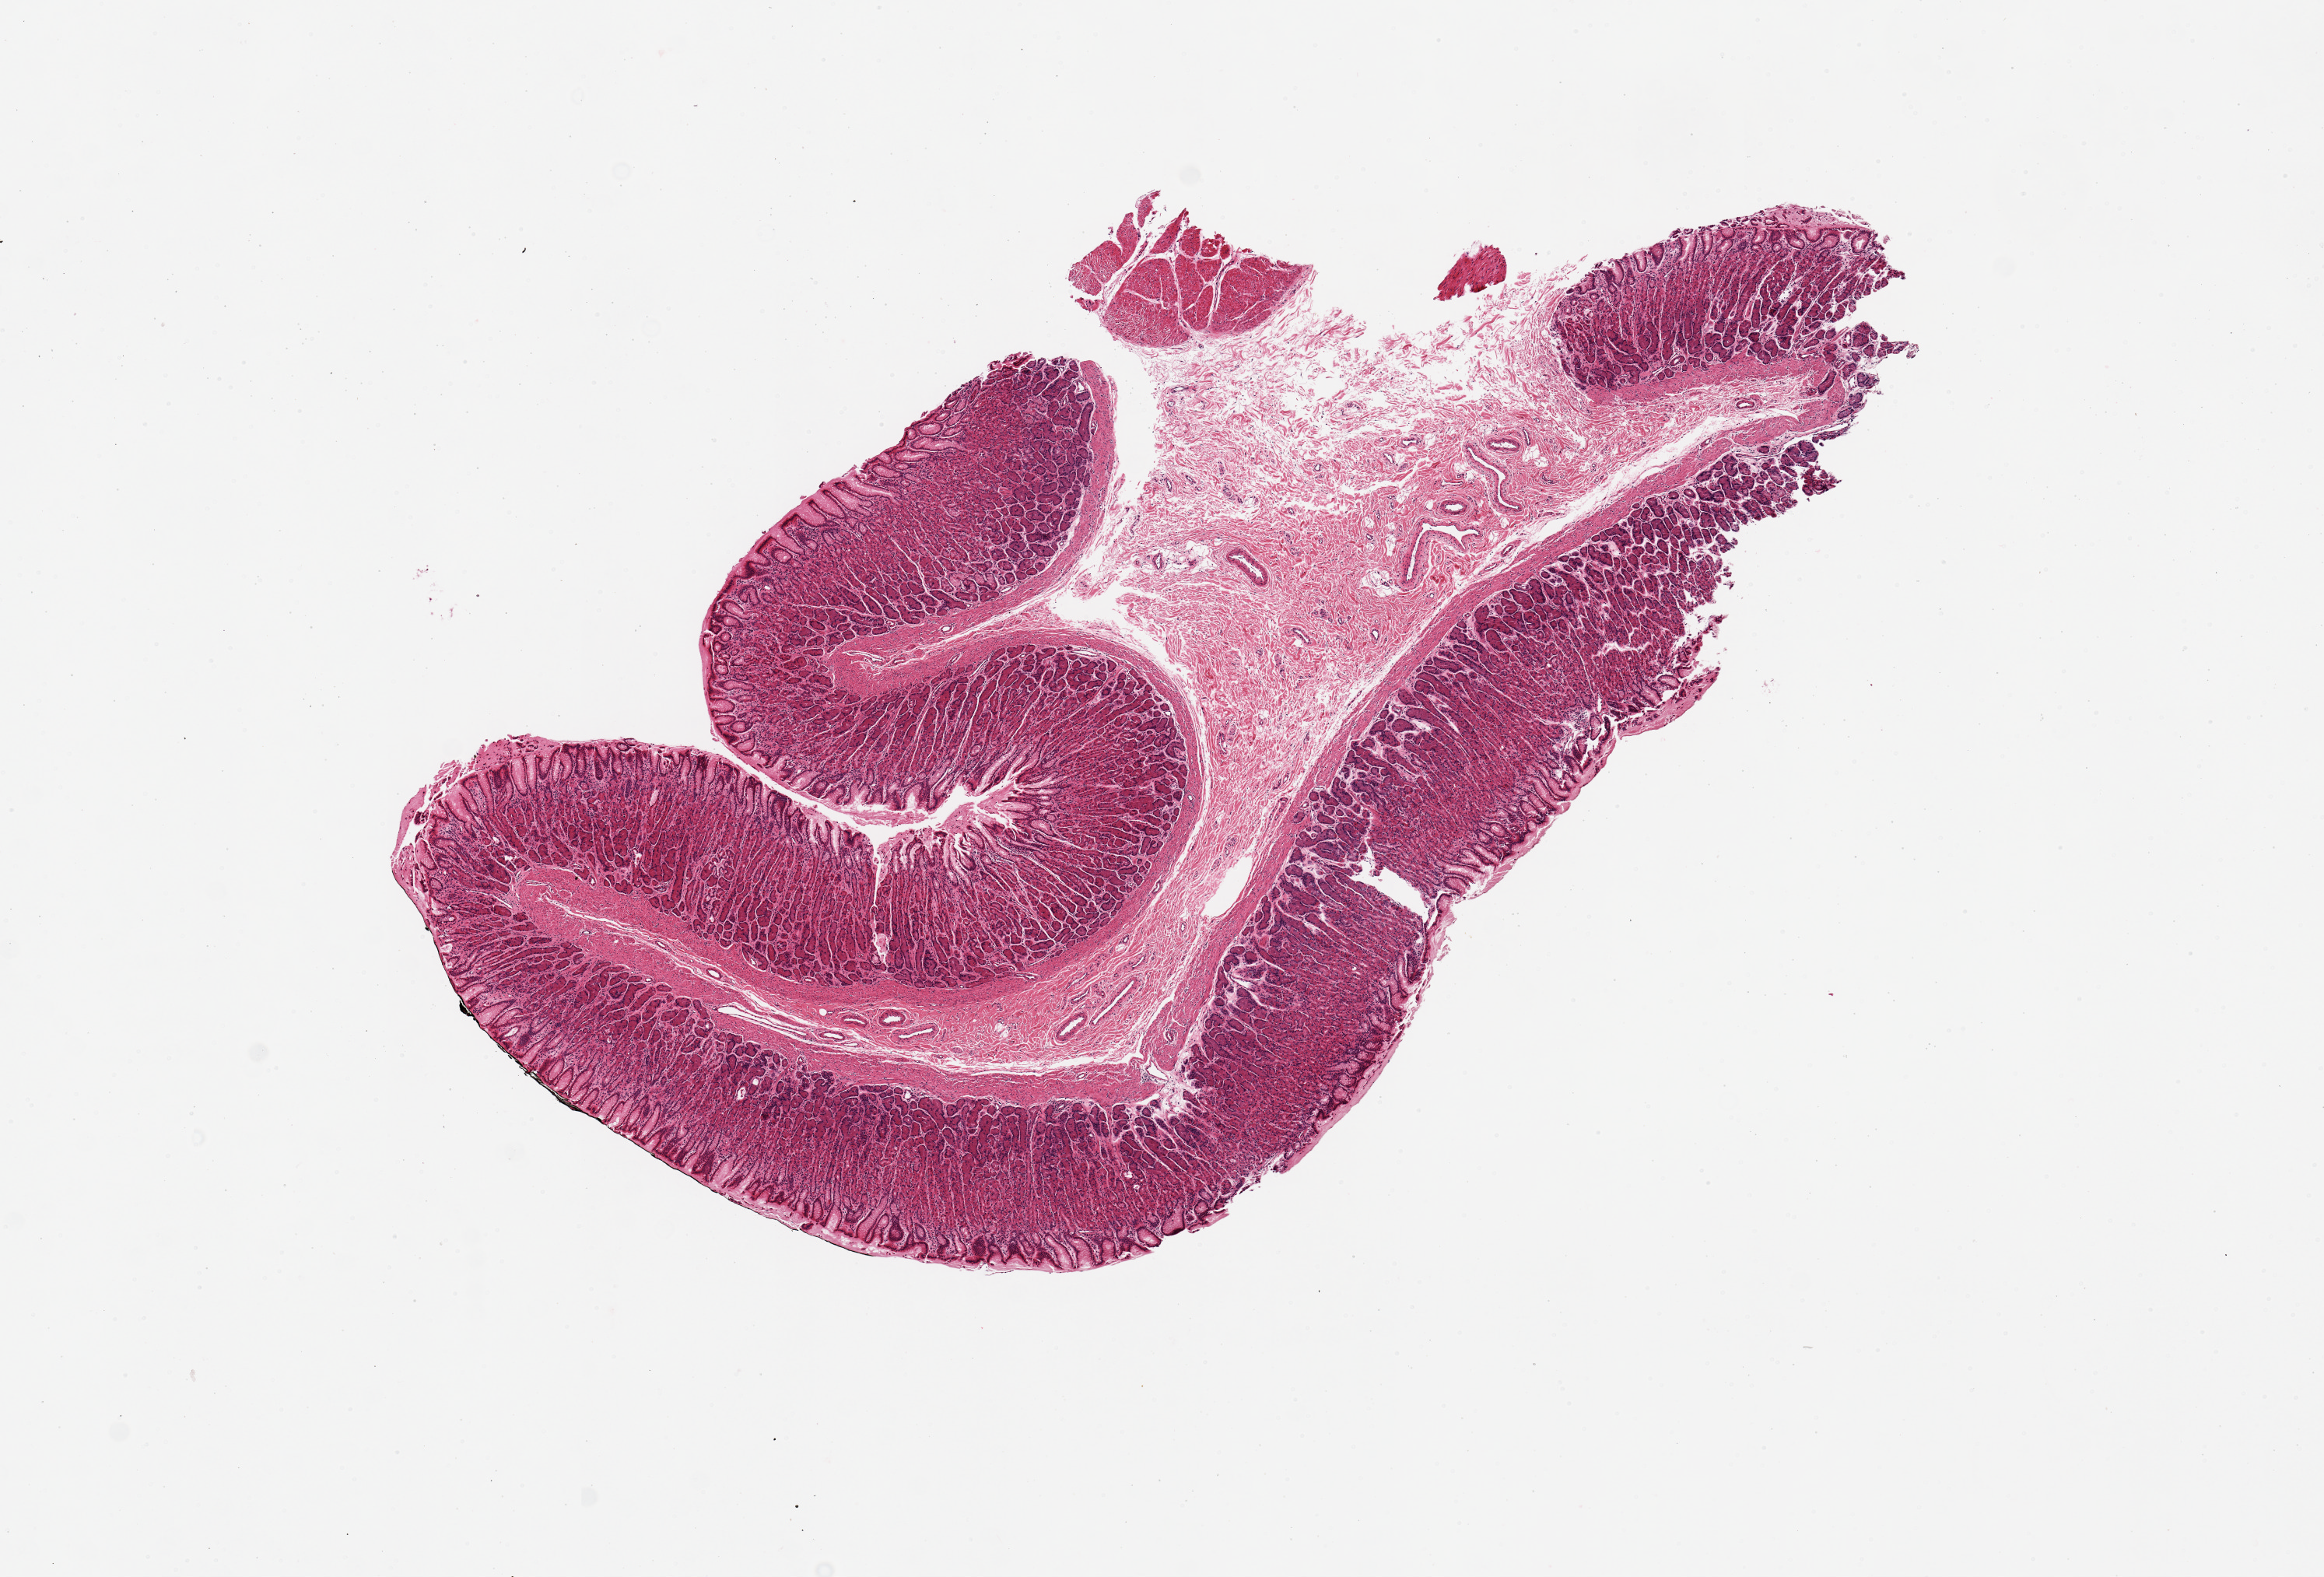
Digitized H&E-stained section — shown as a low-resolution overview of the whole scanned area (about 11.8 x 8.0 mm). PAXgene-fixed, paraffin-embedded tissue. Section of stomach (target tissue). Donor tissue sample.
Review note (as recorded): 1 piece, 7x5mm; mucoa well - preserved, up to 1mm thick.